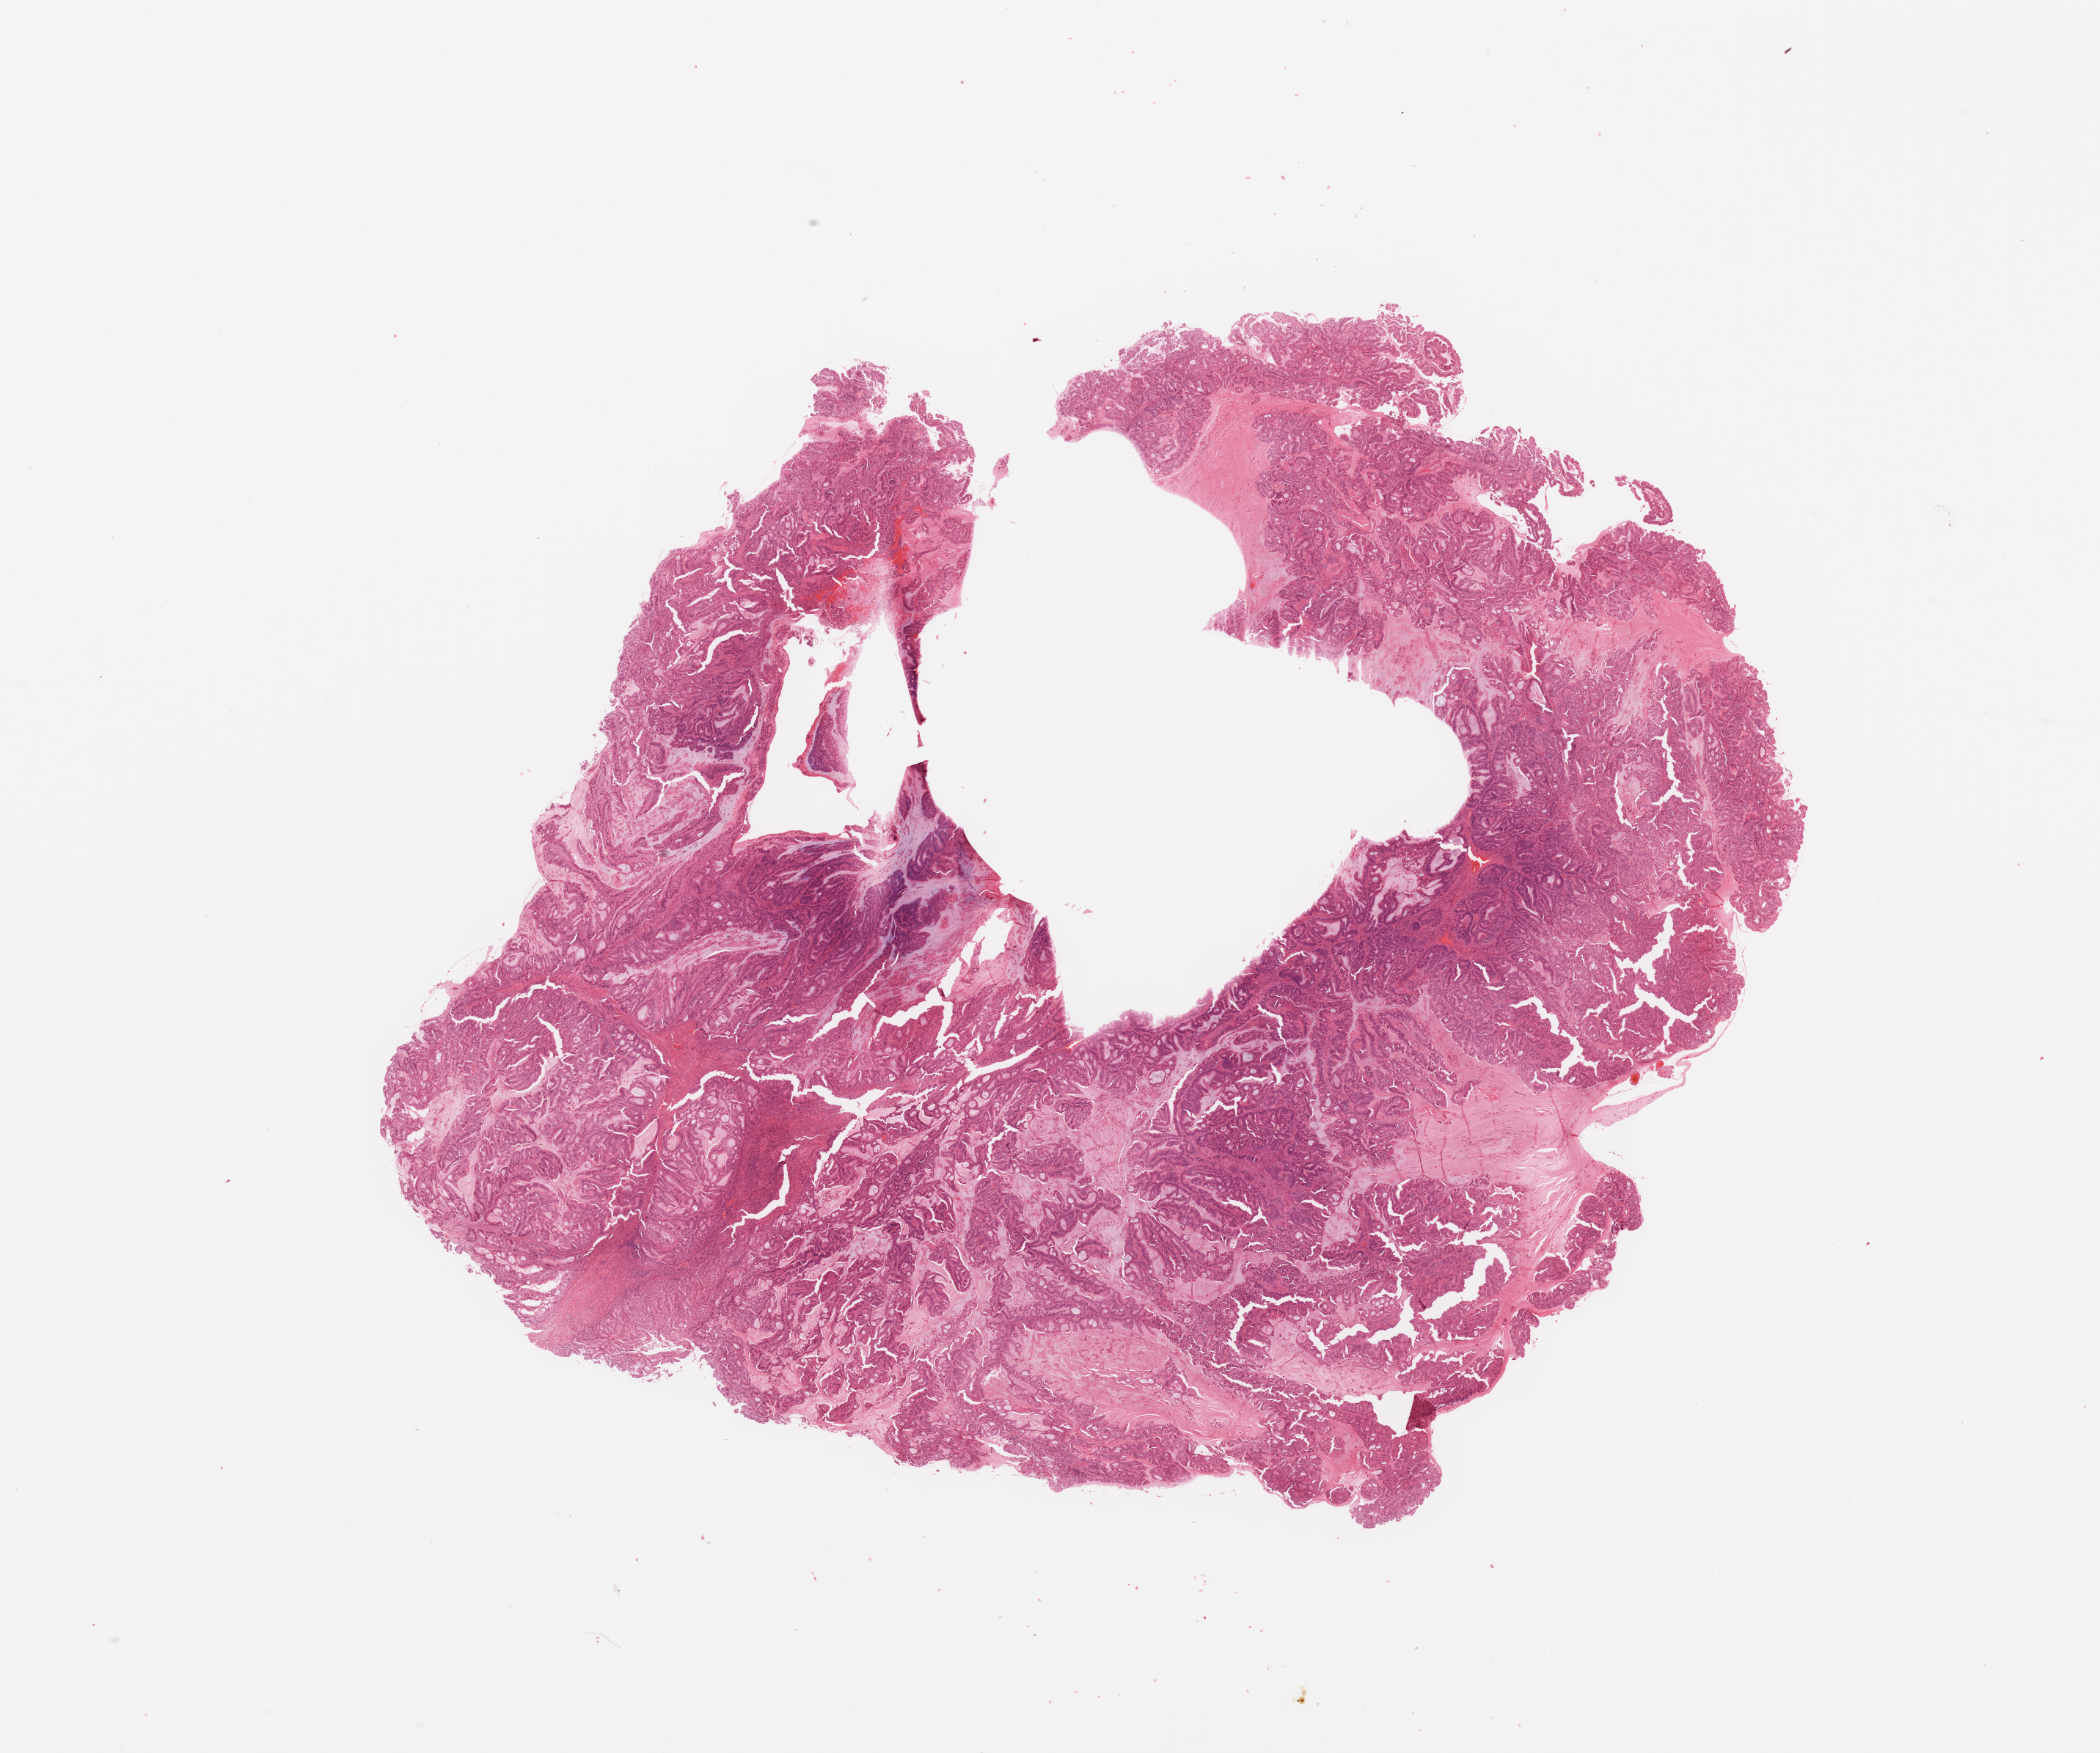
Digitized Hematoxylin and eosin (H&E) stained tissue section (whole slide), whole scanned area (about 22.6 x 18.9 mm, from a 20x scan) shown as a low-resolution overview, tumour tissue sample, sampled site: uterus. Patient: female, age 77 years. Histologic grade: G1 (well differentiated). Slide review estimates, as recorded: tumour nuclei 85%, necrosis 0%.
Diagnosis: Endometrioid adenocarcinoma, NOS.